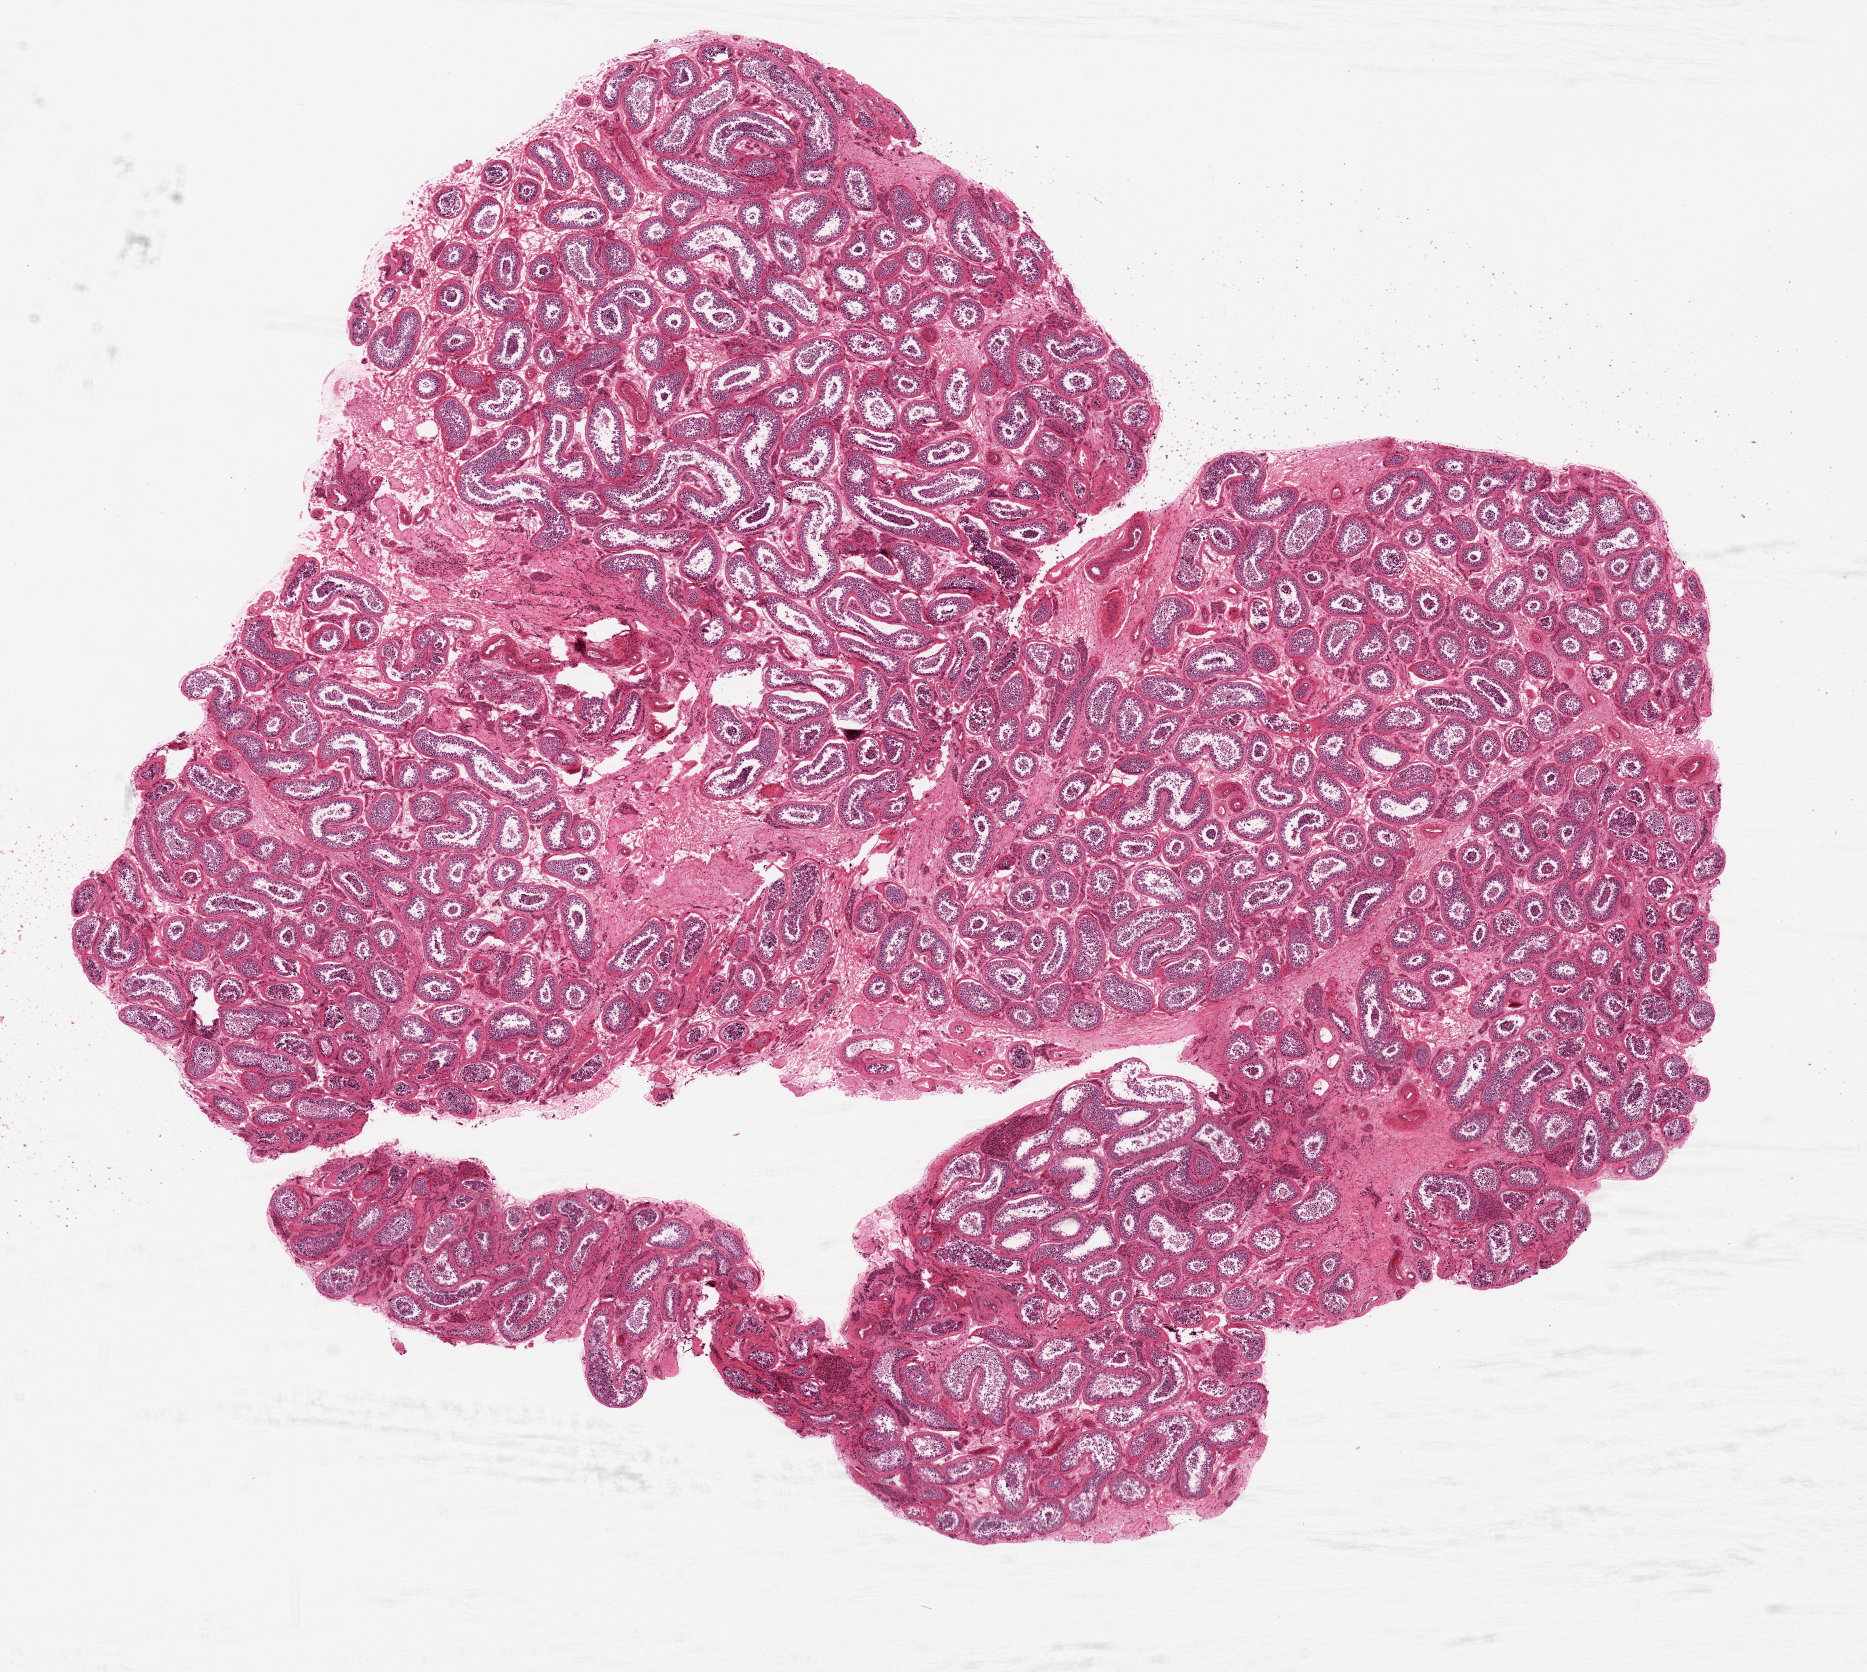
Haematoxylin and eosin whole-slide image, whole scanned area (about 14.8 x 13.2 mm, acquisition: 20x scan) shown as a low-resolution overview; PAXgene-fixed paraffin-embedded (PFPE) section; section of testis (target tissue); tissue donor sample. Donor: male.
Review note (as recorded): 12 x 8.8mm. Good spermatogenesis evident.